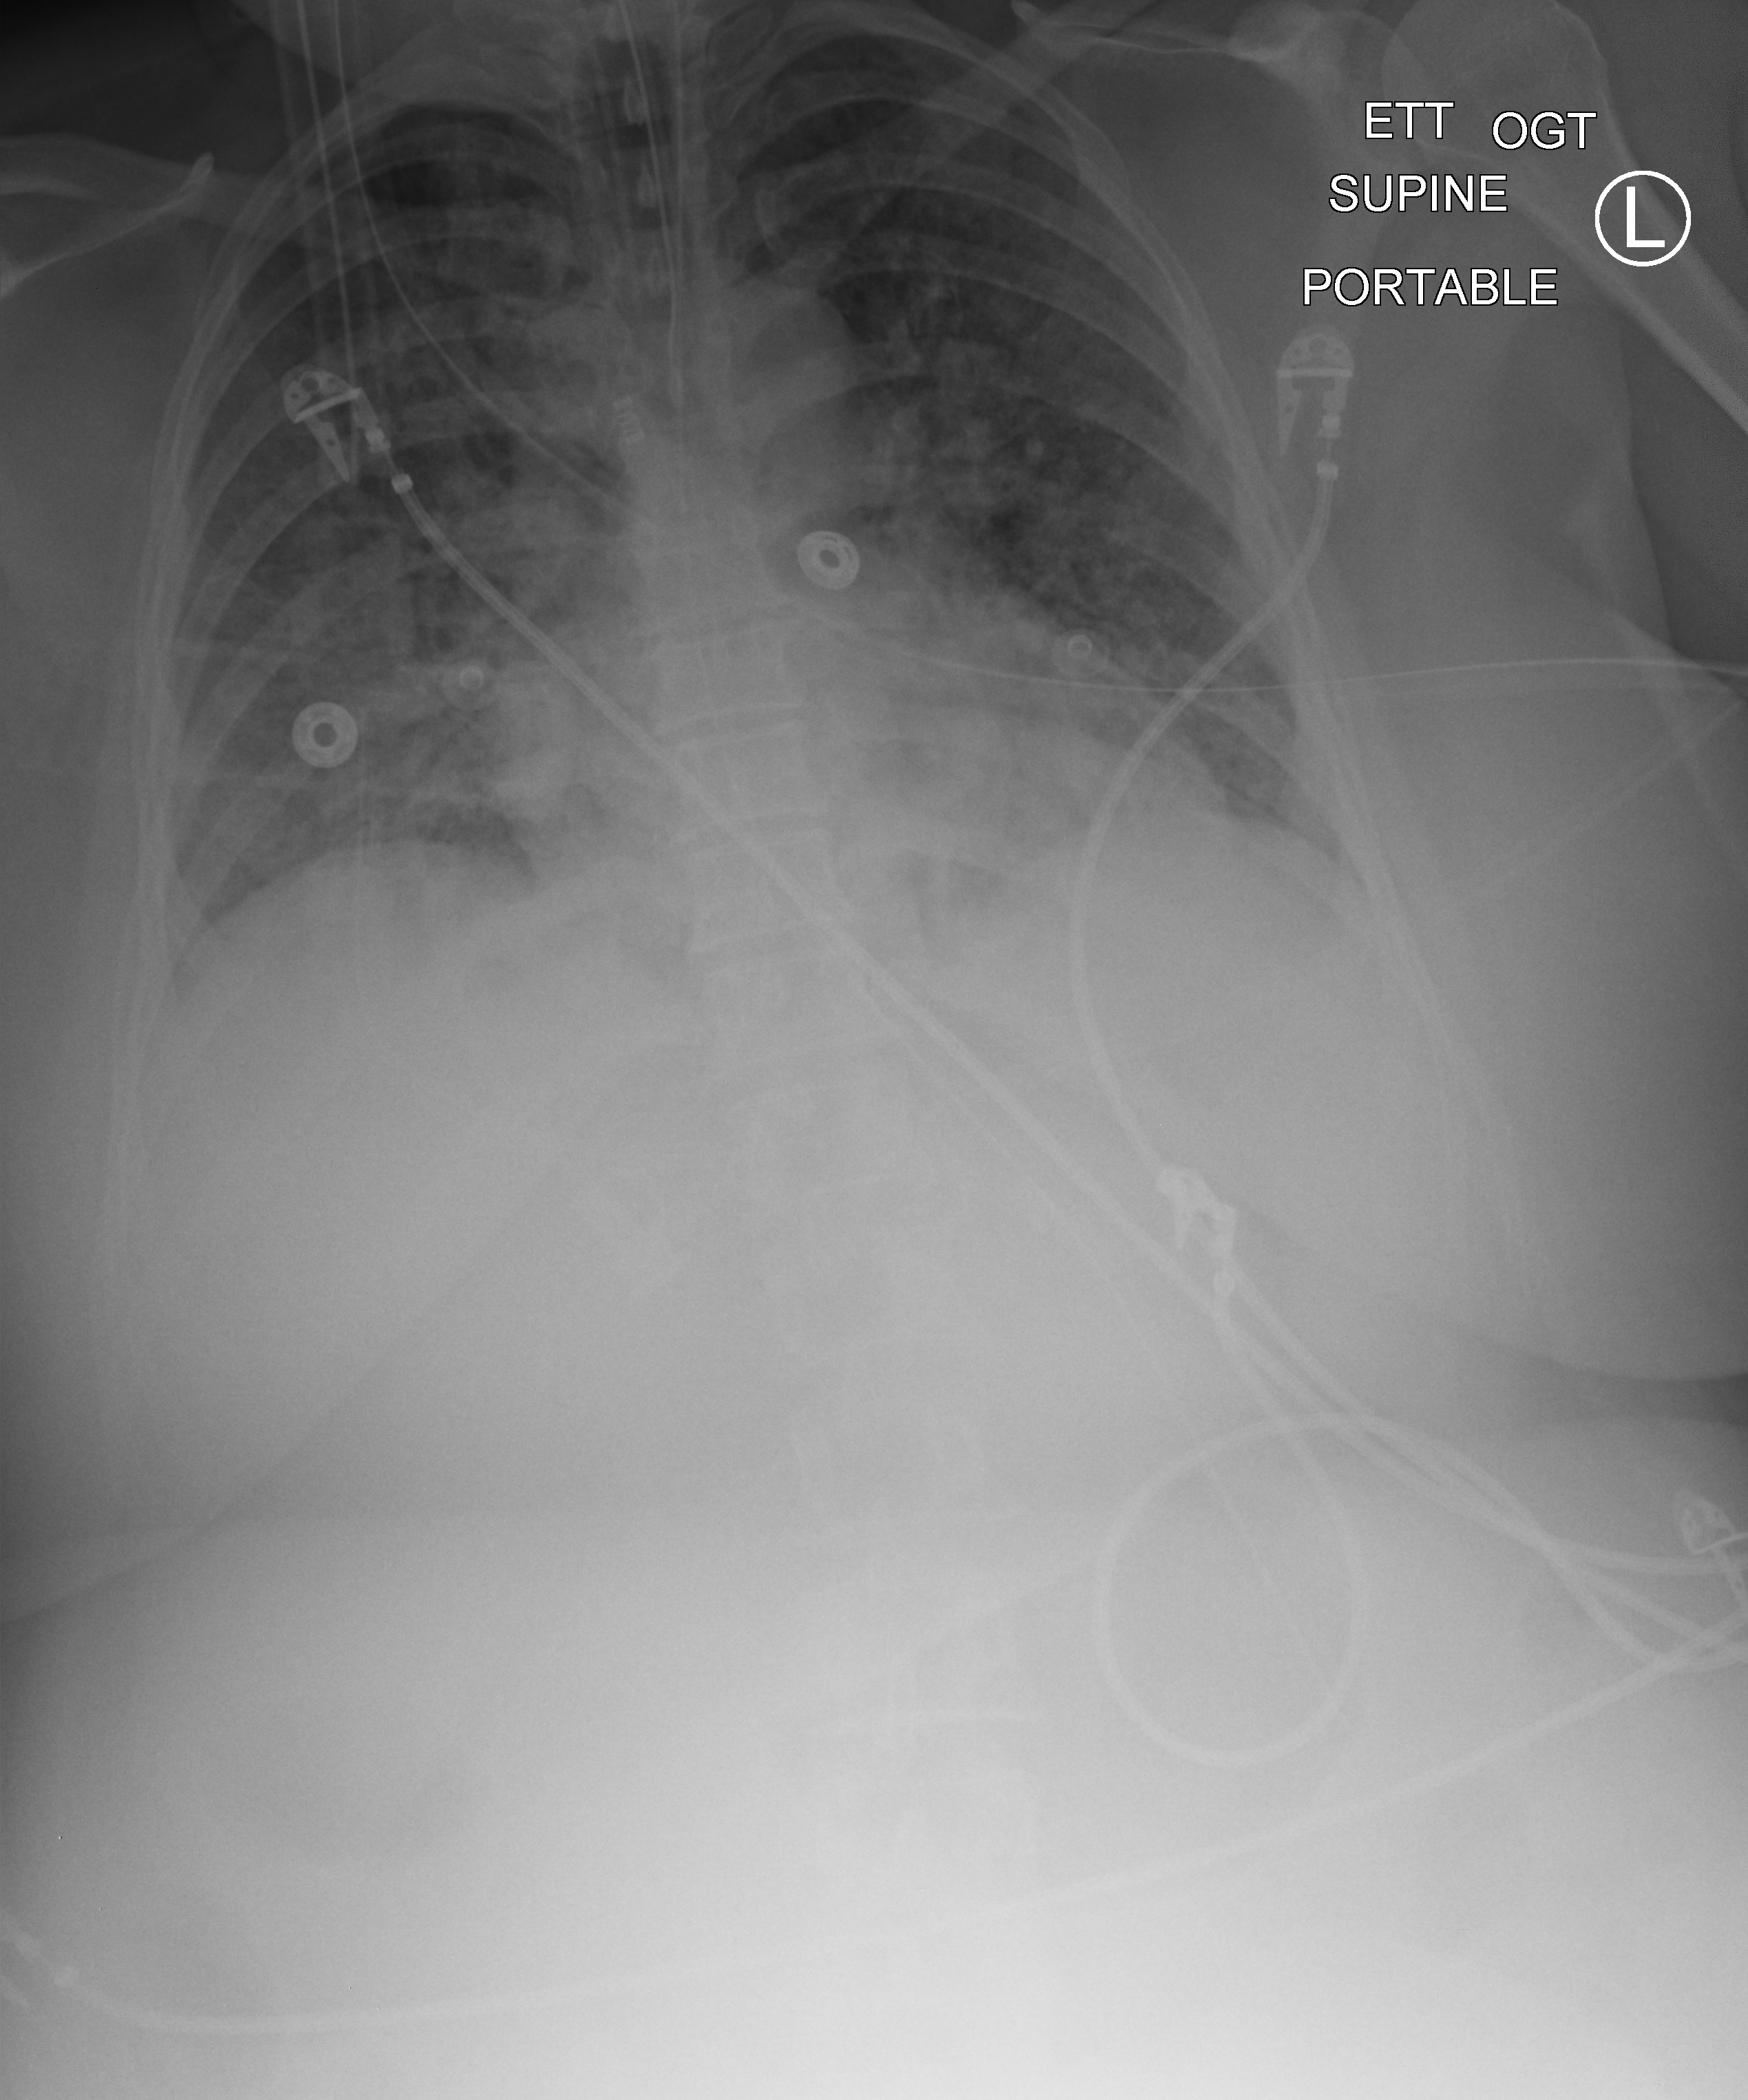
Portable chest radiograph; anteroposterior (AP) projection. Patient hospitalised with COVID-19; female, aged 18–59 years.
From the hospital-stay record, not from the radiograph (when in the stay this image was taken is not recorded):
- mechanically ventilated during this hospital stay: yes
- chronic kidney disease (admission record): no